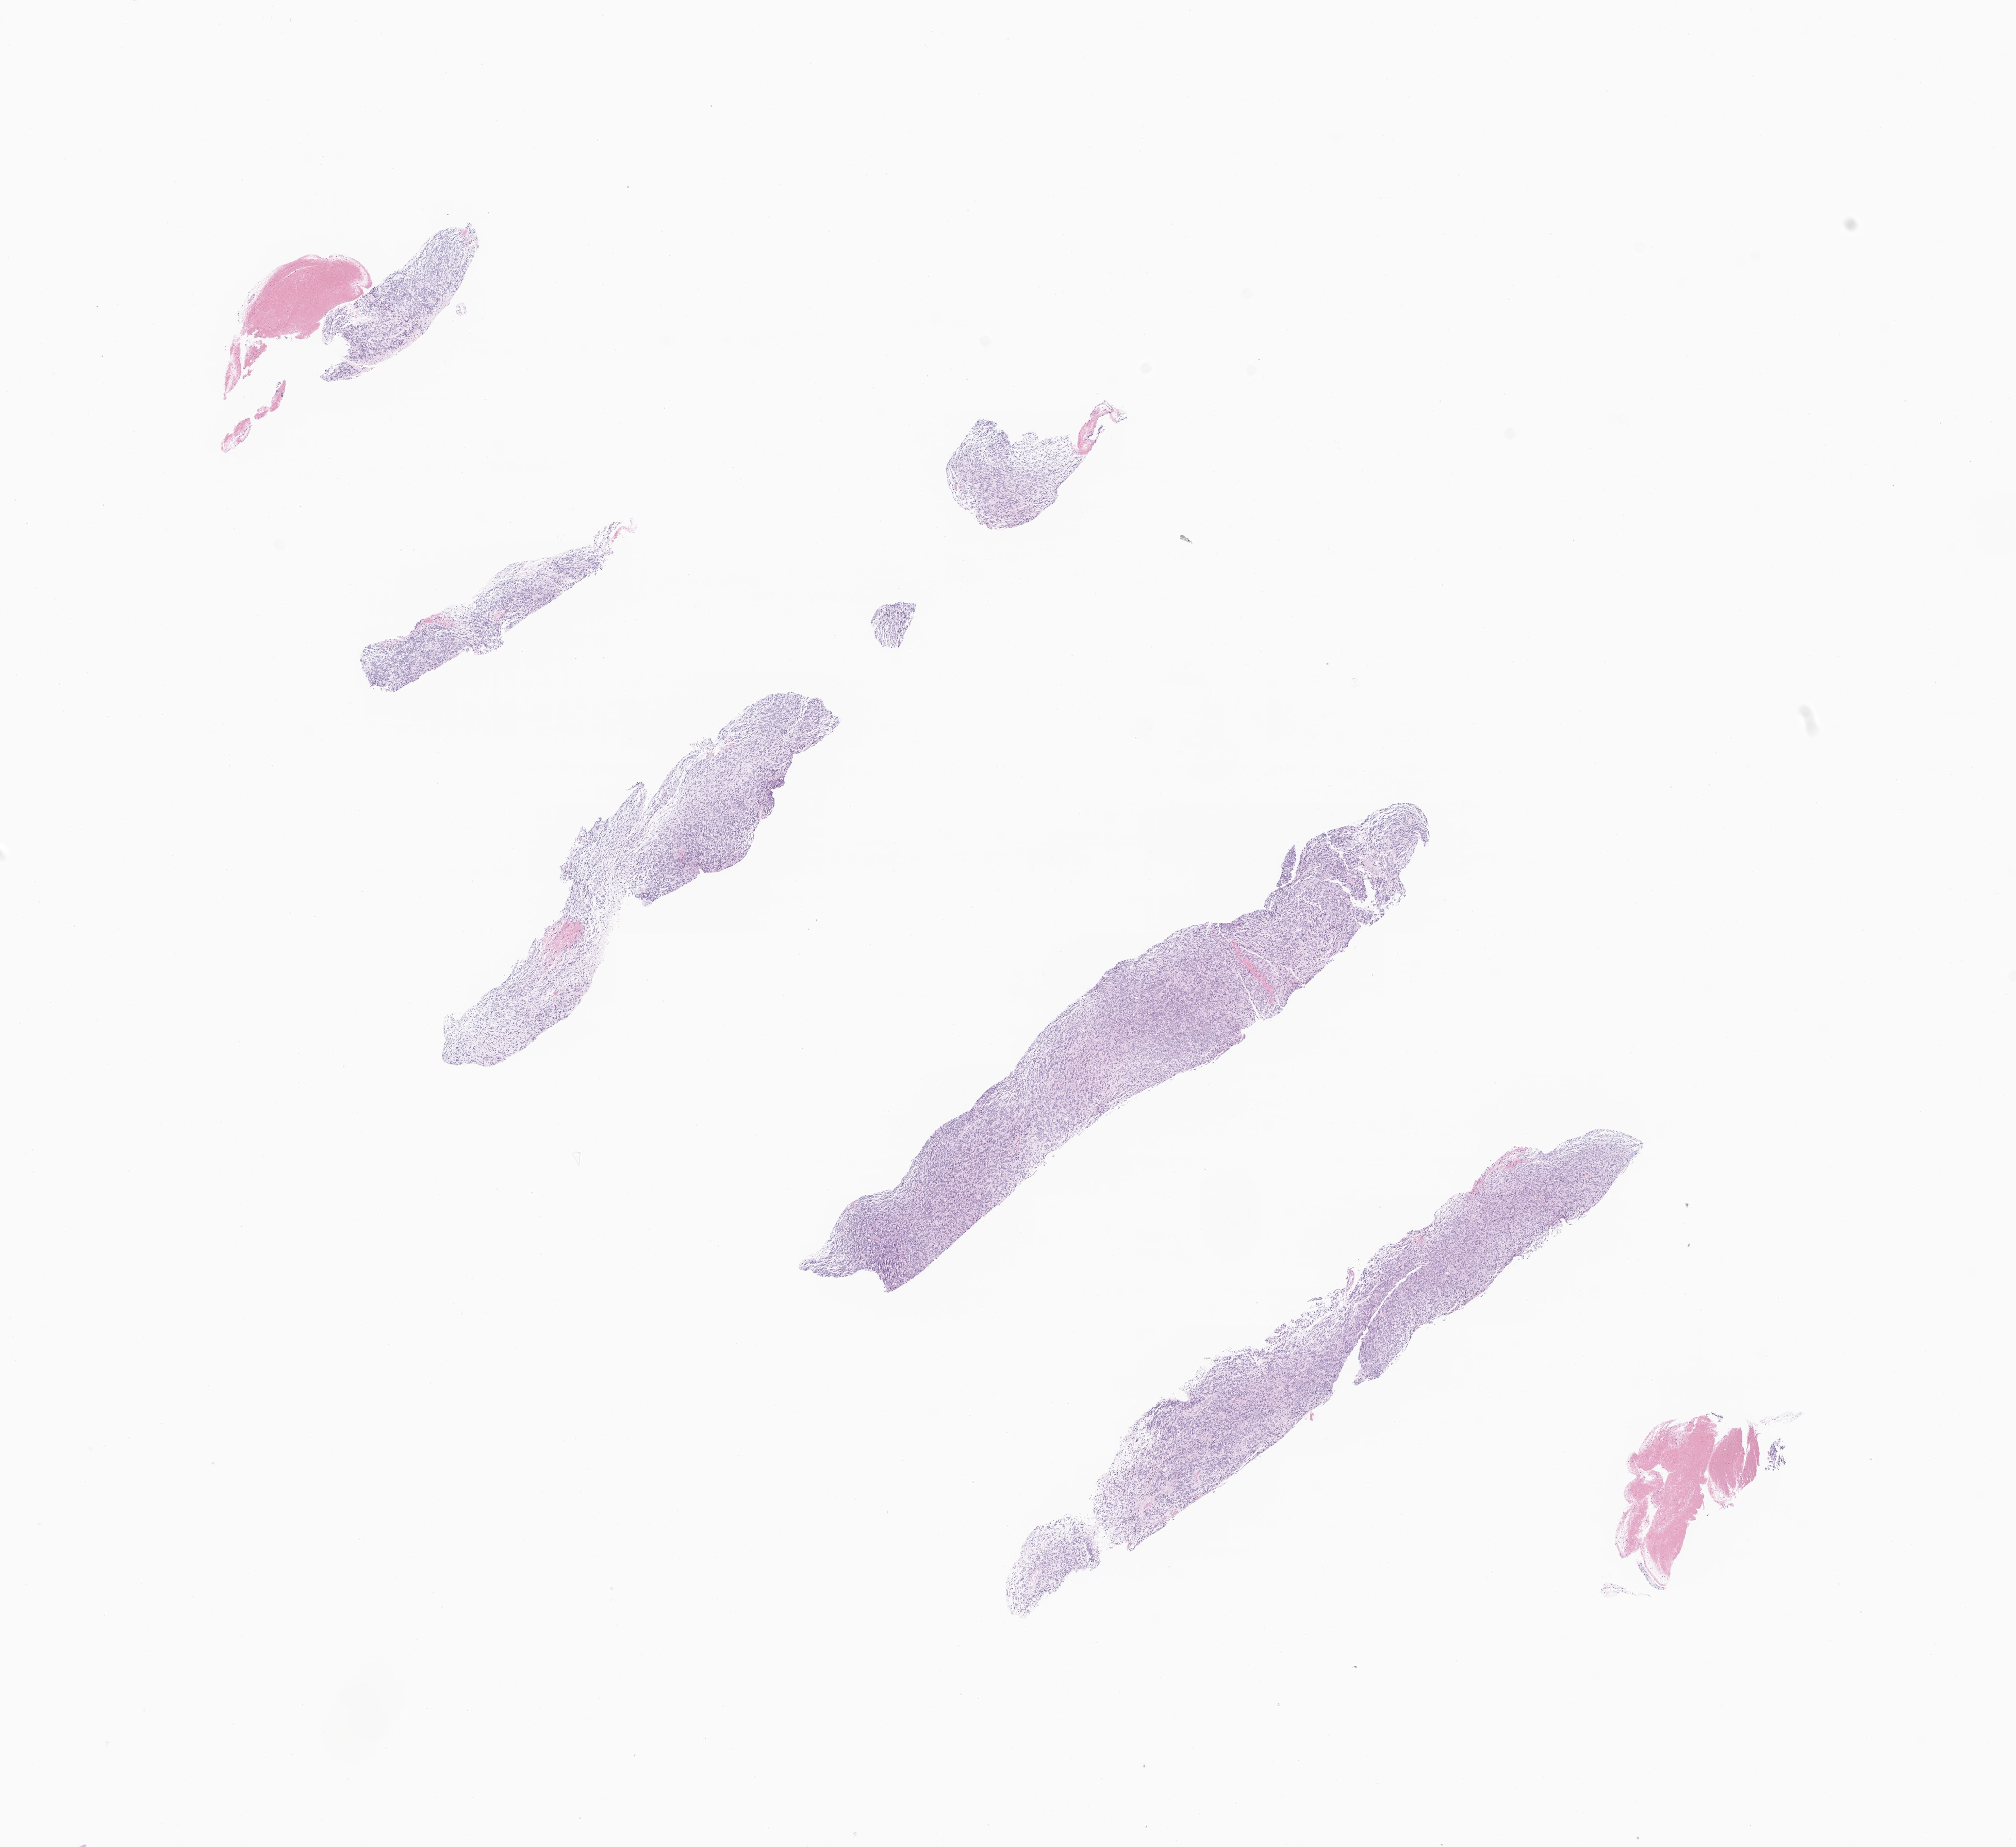
Hematoxylin and eosin (H&E) whole-slide image of tumor tissue from the brain stem, shown as a low-resolution overview of the whole scanned area (about 16.5 x 15.1 mm). Formalin-fixed, paraffin-embedded (FFPE) tissue. Female patient, age 145 months (12 years 1 month).
Diagnosis (ICD-O-3 morphology term): Glioma, malignant.